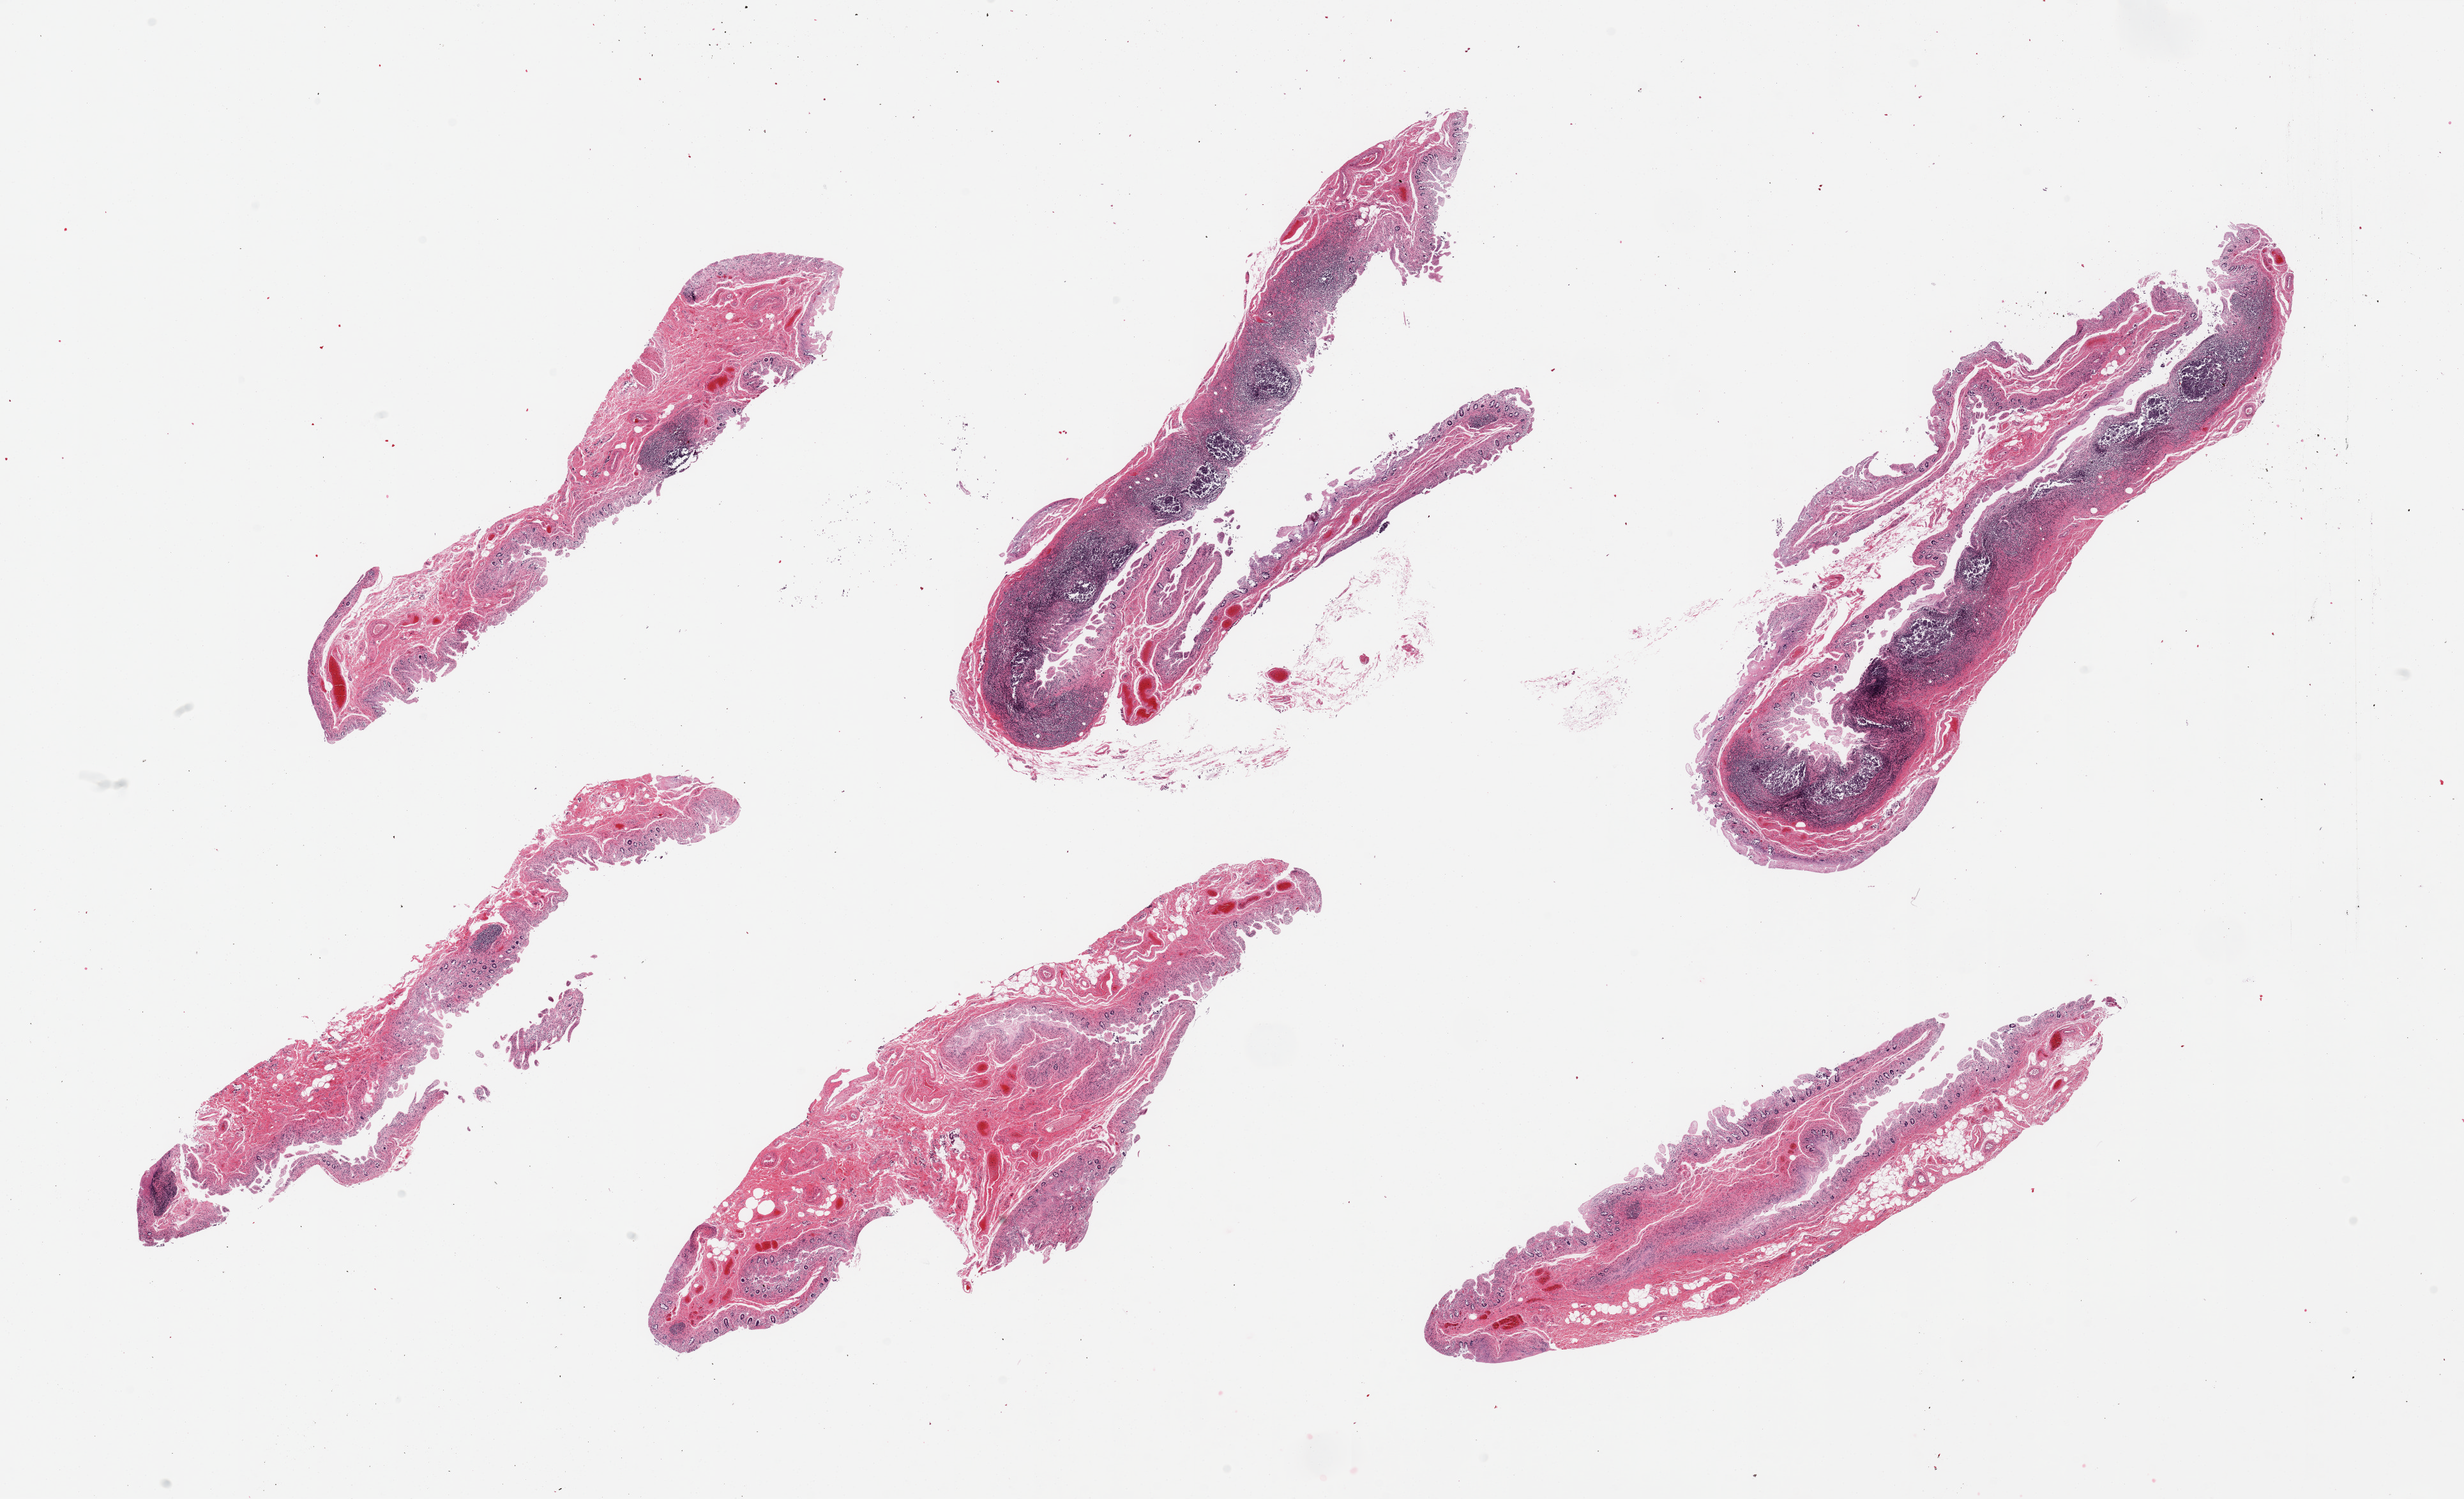
Hematoxylin and eosin (H&E) whole-slide image, shown as a low-resolution overview of the whole scanned area (about 30.5 x 18.6 mm, slide scanned at 20x); PAXgene-fixed, paraffin-embedded tissue; section of ileum (target tissue); donor tissue sample. Female donor.
Review note (as recorded): 6 pieces; autolyzed mucosa with residual lymphoid nodules (some).